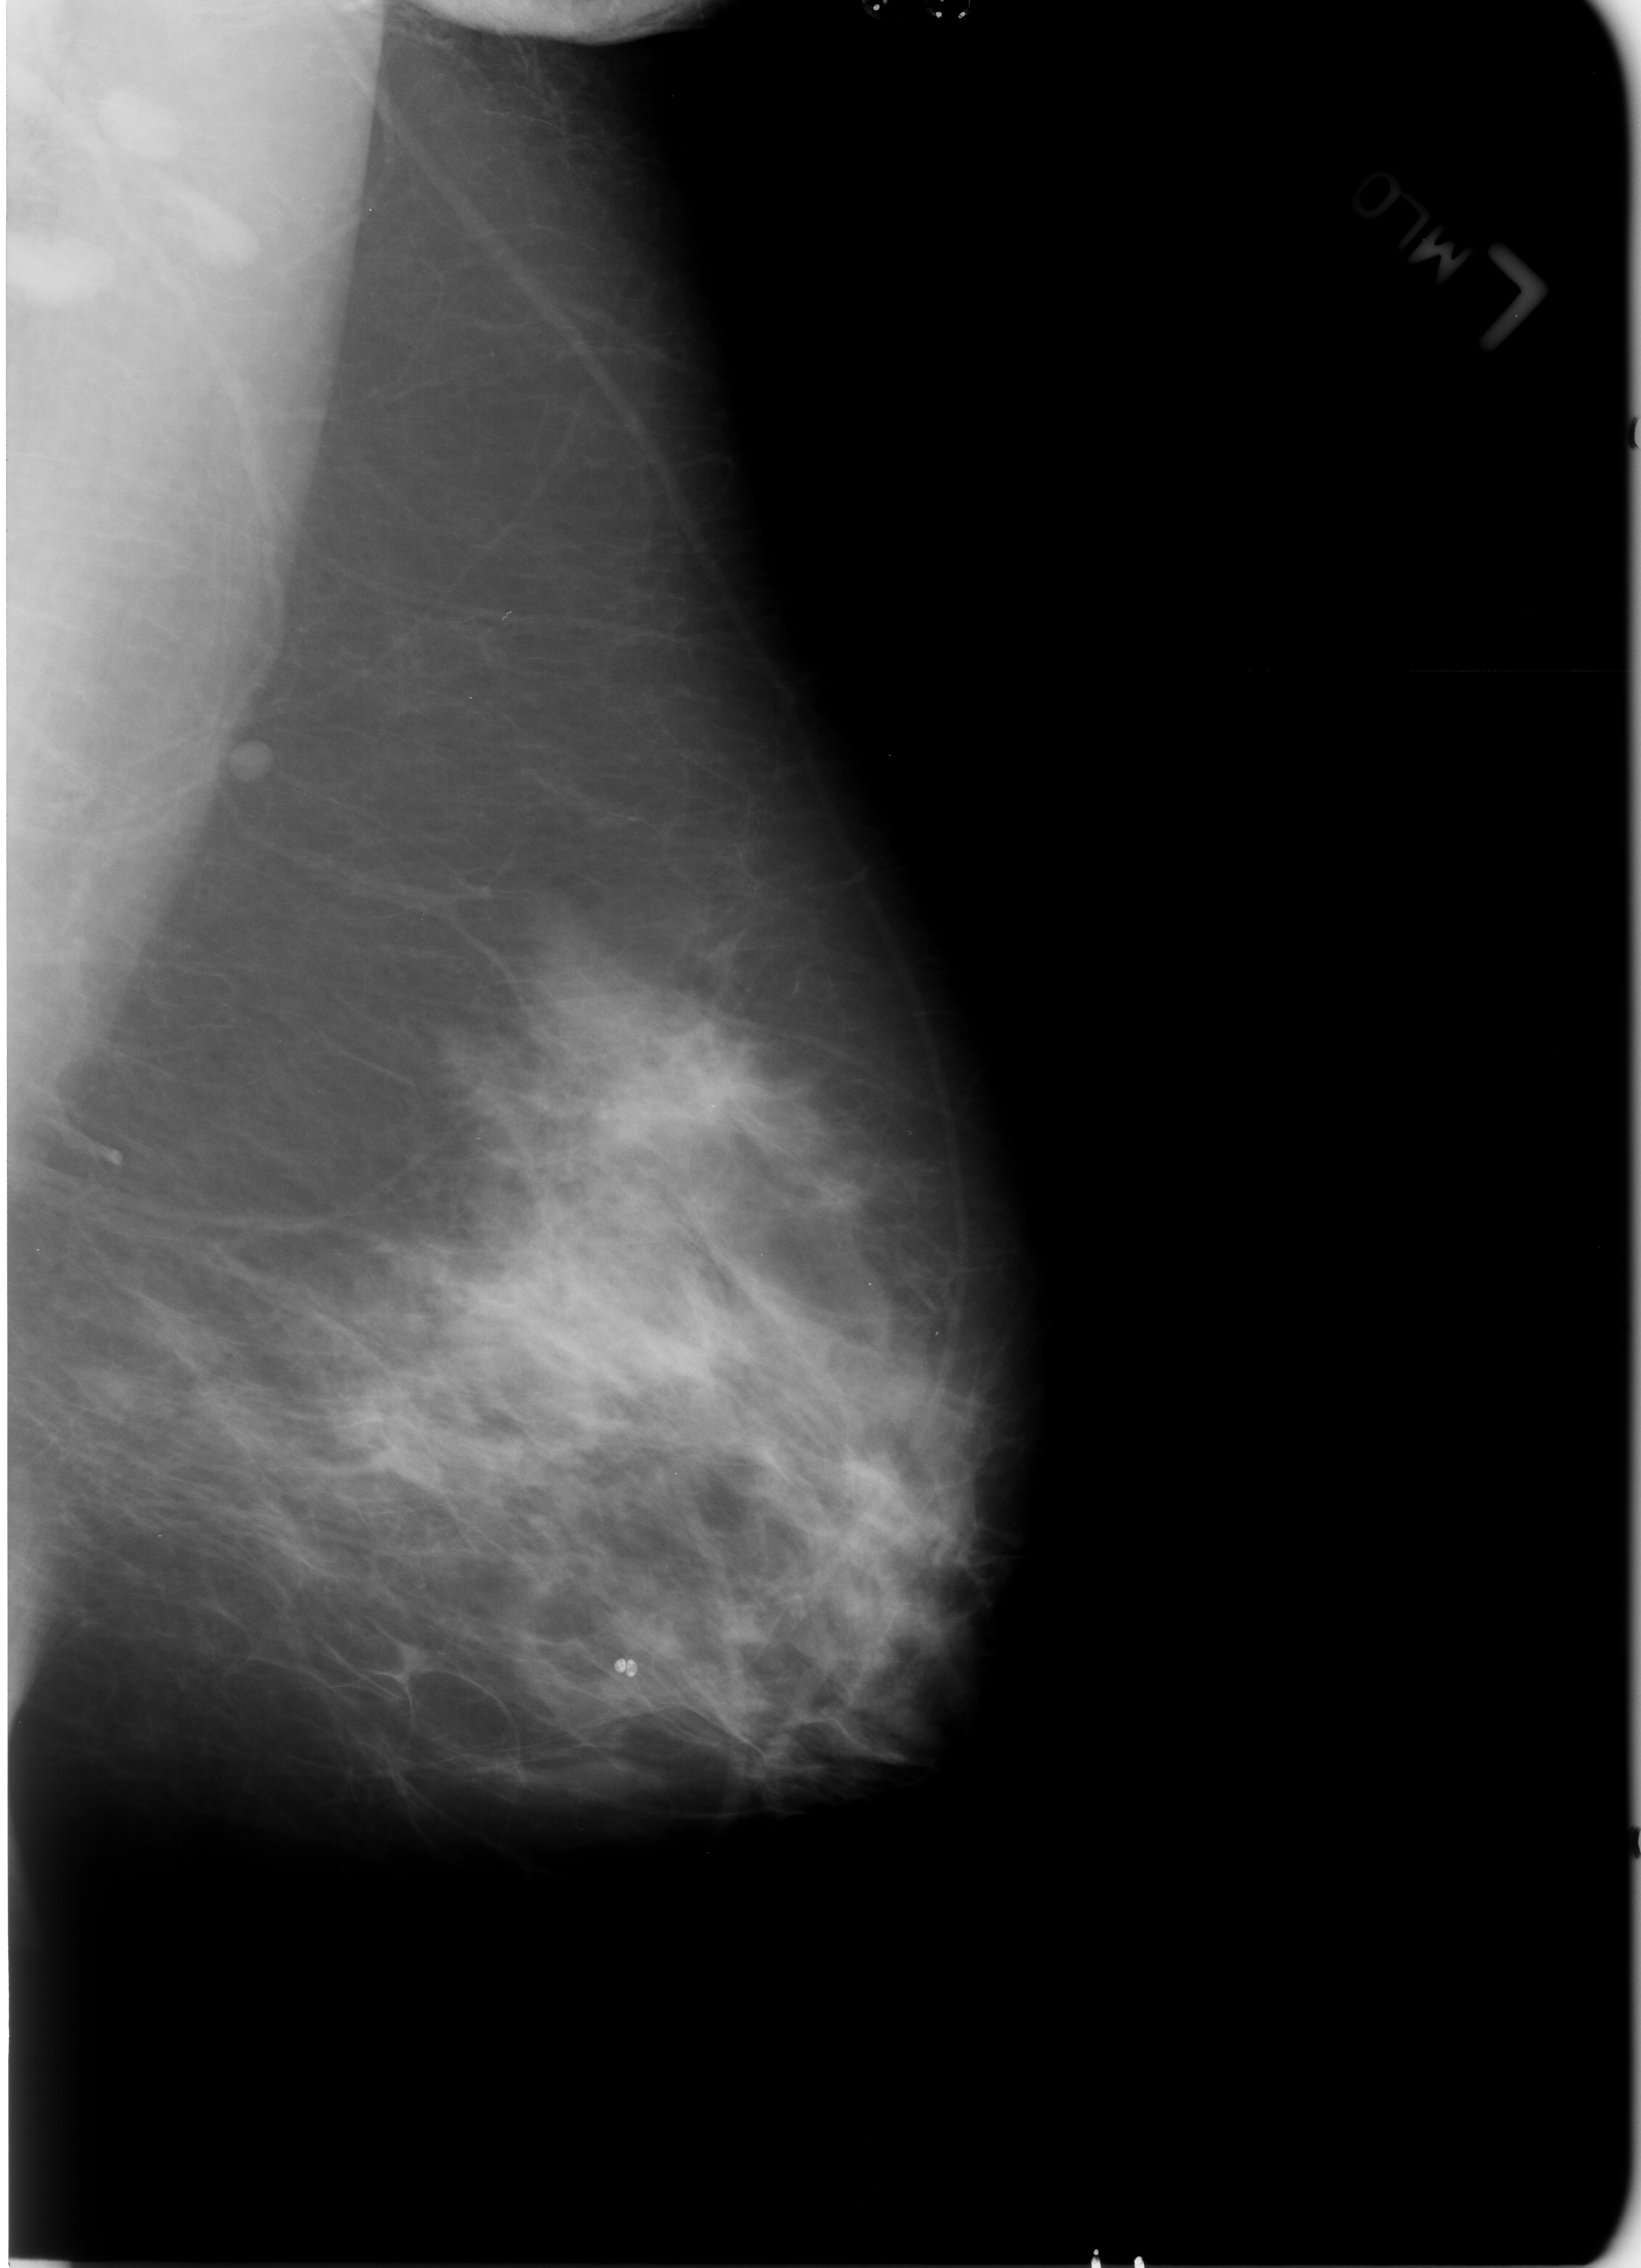
Mammogram (digitized film); left breast; mediolateral oblique (MLO) view; BI-RADS breast density category 3 (scale 1–4); 1641 × 2268 image matrix.
Expert-marked regions of interest on this film, with their recorded descriptors:
- calcifications, morphology lucent center; BI-RADS assessment category 2; subtlety rating 3 on a 1 (subtle) to 5 (obvious) scale; benign; no additional work-up was recommended (outcome (as recorded, no biopsy): benign without callback): box from (x=610, y=1647) to (x=650, y=1693) px